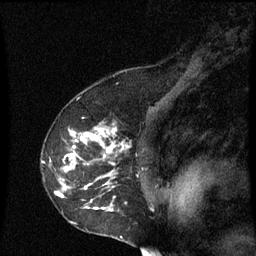
Breast MRI (dynamic contrast-enhanced), one sagittal slice. Position 44 of 60 along the scan axis. Dynamic contrast-enhanced series, image 2 of 3 at this slice position (ordered by acquisition). 1.5 T. TE 4.2 ms, TR 8.9 ms. 2 mm slice thickness. 256 × 256 image matrix. Female patient, age 53 years. Case-level facts recorded for this patient, not image findings: setting: breast cancer imaged before/during neoadjuvant chemotherapy; receptor status: HR-positive, HER2-negative.
Outlined on this slice (semi-automatically segmented with operator editing):
- analysis volume of interest (the breast-tissue region the enhancement analysis was run in; not a lesion): bounding box (x1, y1, x2, y2) in pixels: (42, 128, 129, 229)
- tumour enhancement mask (voxels above the 70 % enhancement threshold inside the analysis volume of interest): (56, 128, 123, 211)